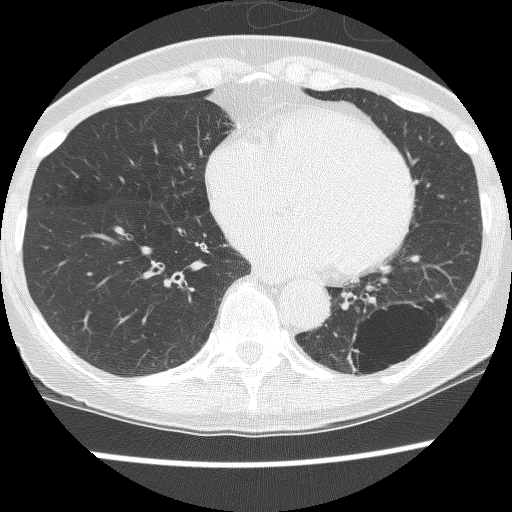
Chest CT (low-dose screening protocol), one axial image, third annual screen, lung window (W 1500 / L -600 HU), 2.5 mm slice thickness, lung (sharp) reconstruction kernel (BONE), slice 84 of 130 in the series. Female participant, aged 61 years at enrolment. Current smoker at enrolment.
Expert-annotated lung lesion, bounding box (x1, y1, x2, y2) in pixels: (330, 290, 448, 390). The screening reader recorded 2 non-calcified nodules or masses ≥4 mm on this exam (left lower lobe, left lower lobe); which of them this box marks is not recorded. Later outcome: lung cancer diagnosed 166 days after this screen — non-small cell carcinoma, left lower lobe, poorly differentiated (G3), stage IB (AJCC 6th edition), 100 mm at pathology.